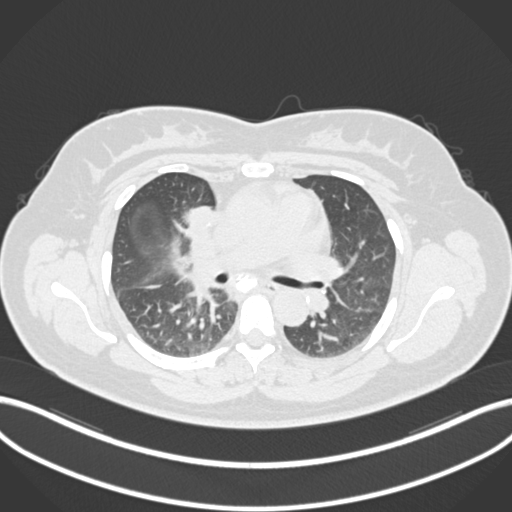
Chest CT, one axial slice. Position 102 of 183 along the scan axis. Reconstruction kernel B30f. 120 kVp. Lung window (W 1500 / L -600 HU). 512 × 512 image matrix, field of view 400 × 400 mm. Patient: female, 46 years. Case-level facts recorded for this patient, not image findings: clinical TNM (as recorded): T2a N1 M0.
Structures marked on this image (rectangle marked by the reading radiologist):
- lung tumour (recorded histology: adenocarcinoma): bounding box [x1, y1, x2, y2] px = [185, 204, 221, 232]